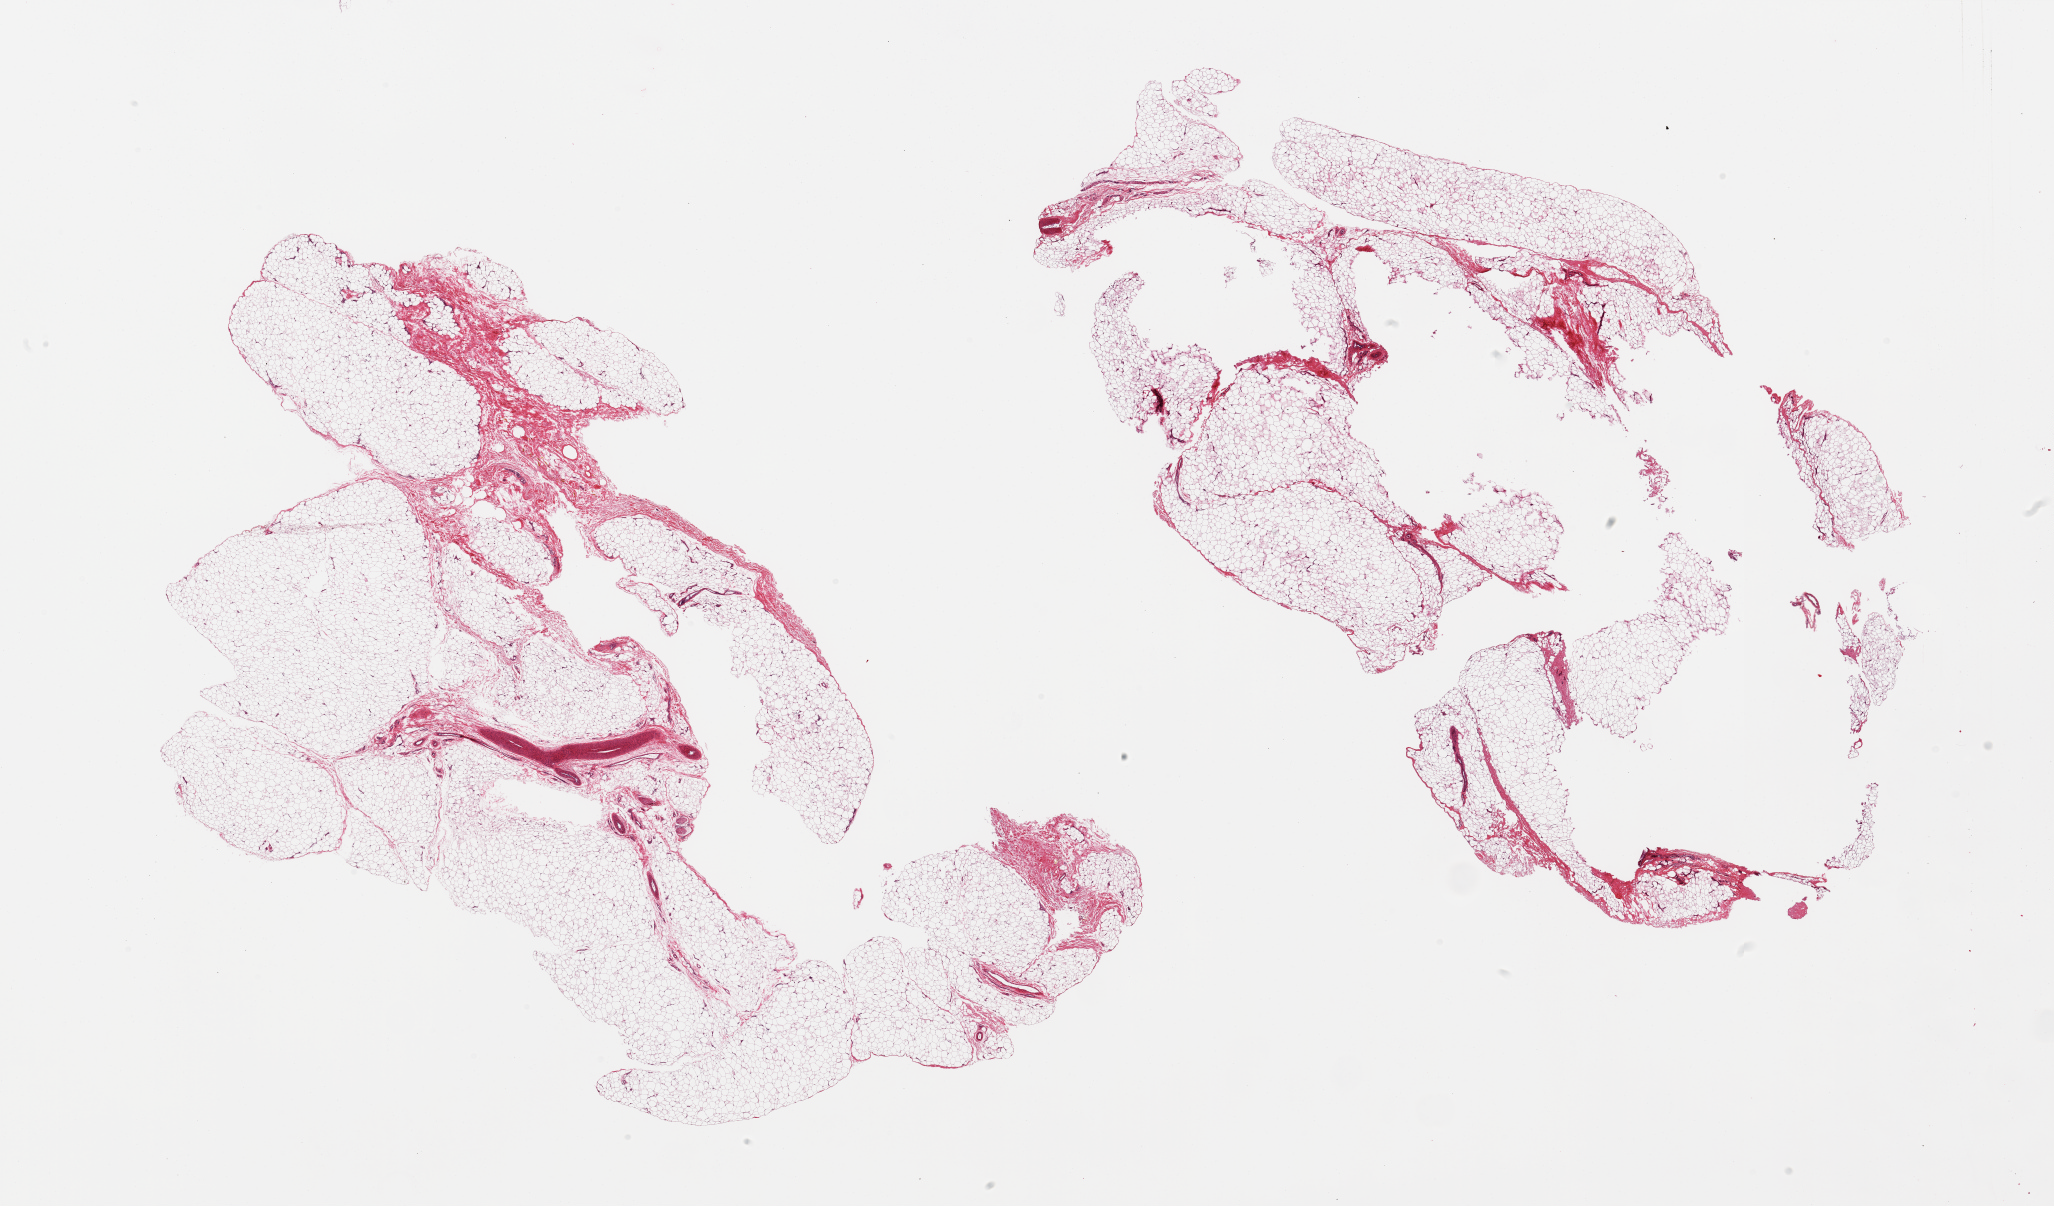
Hematoxylin and eosin (H&E) whole-slide image, low-resolution overview of the scanned area, about 32.5 x 19.1 mm. PAXgene-fixed paraffin-embedded (PFPE) section. Section of adipose tissue (target tissue). Donor tissue sample. Female donor.
Pathologist's review note for this sample: 2 pieces, ~10% fascia/vascular elements.